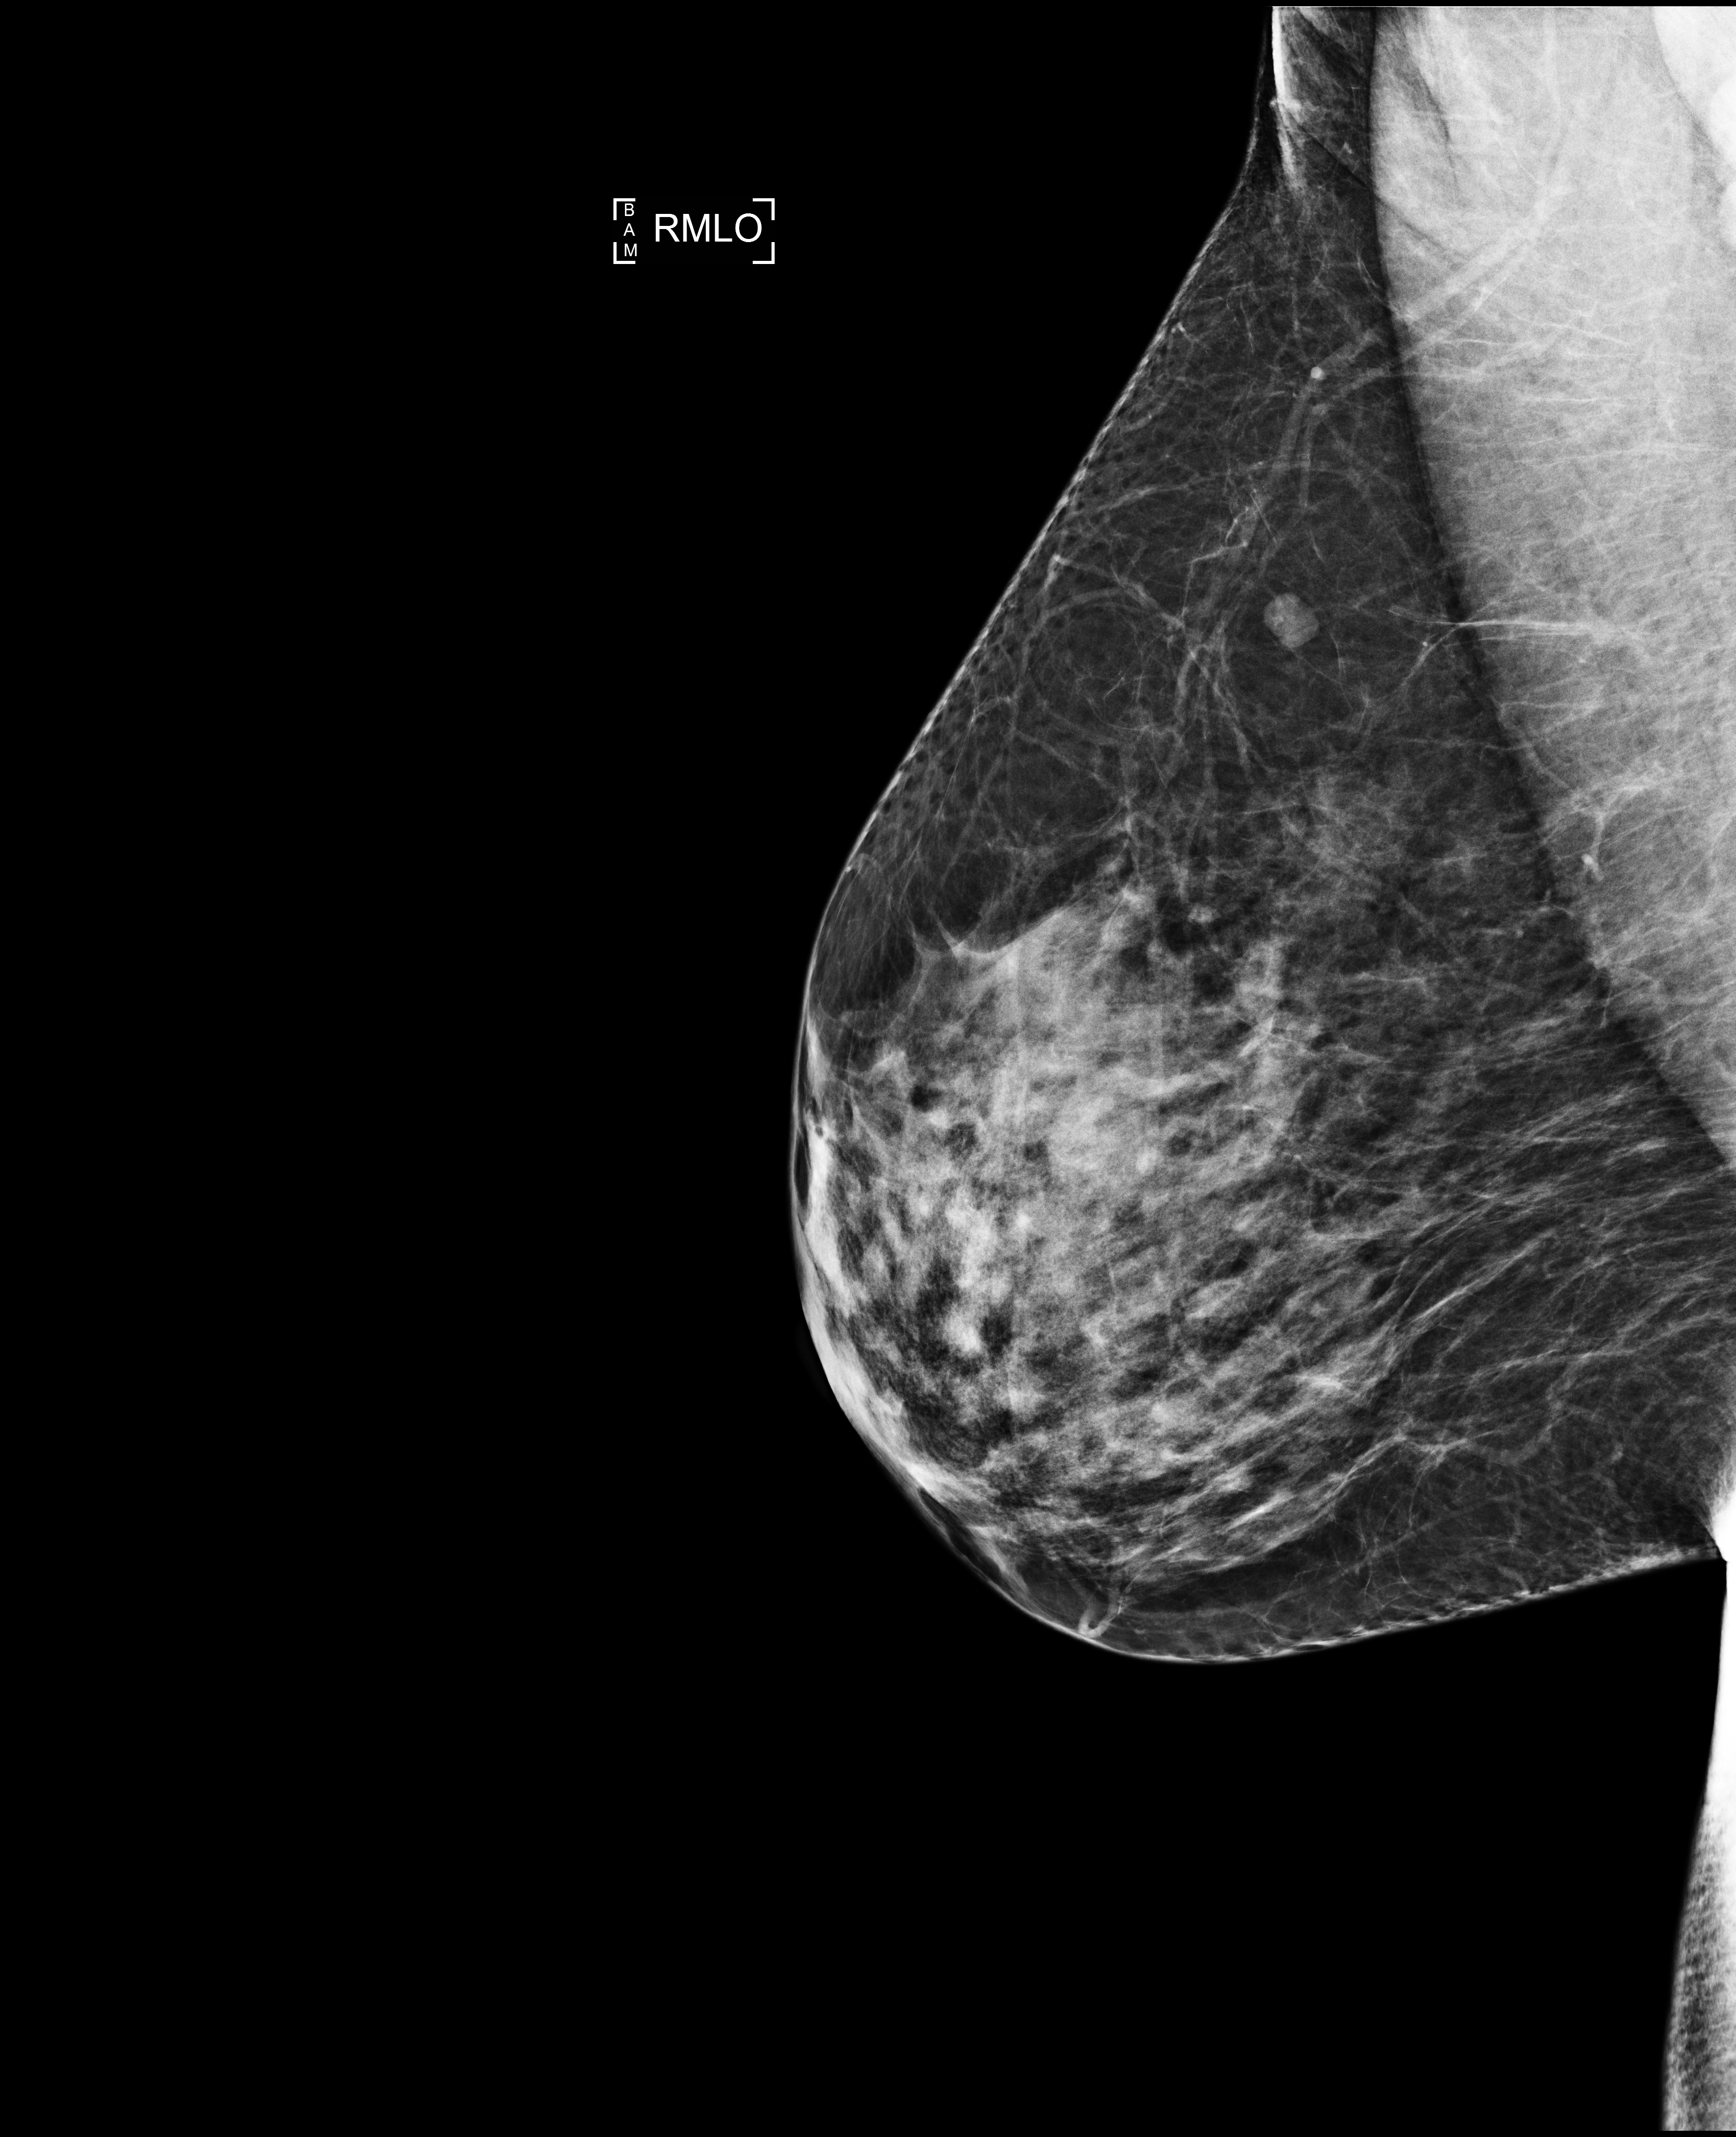
Annual screening mammography examination. Female patient, age 55 years.
Image type: full-field digital mammogram. Breast: right. Projection: mediolateral oblique (MLO) view.